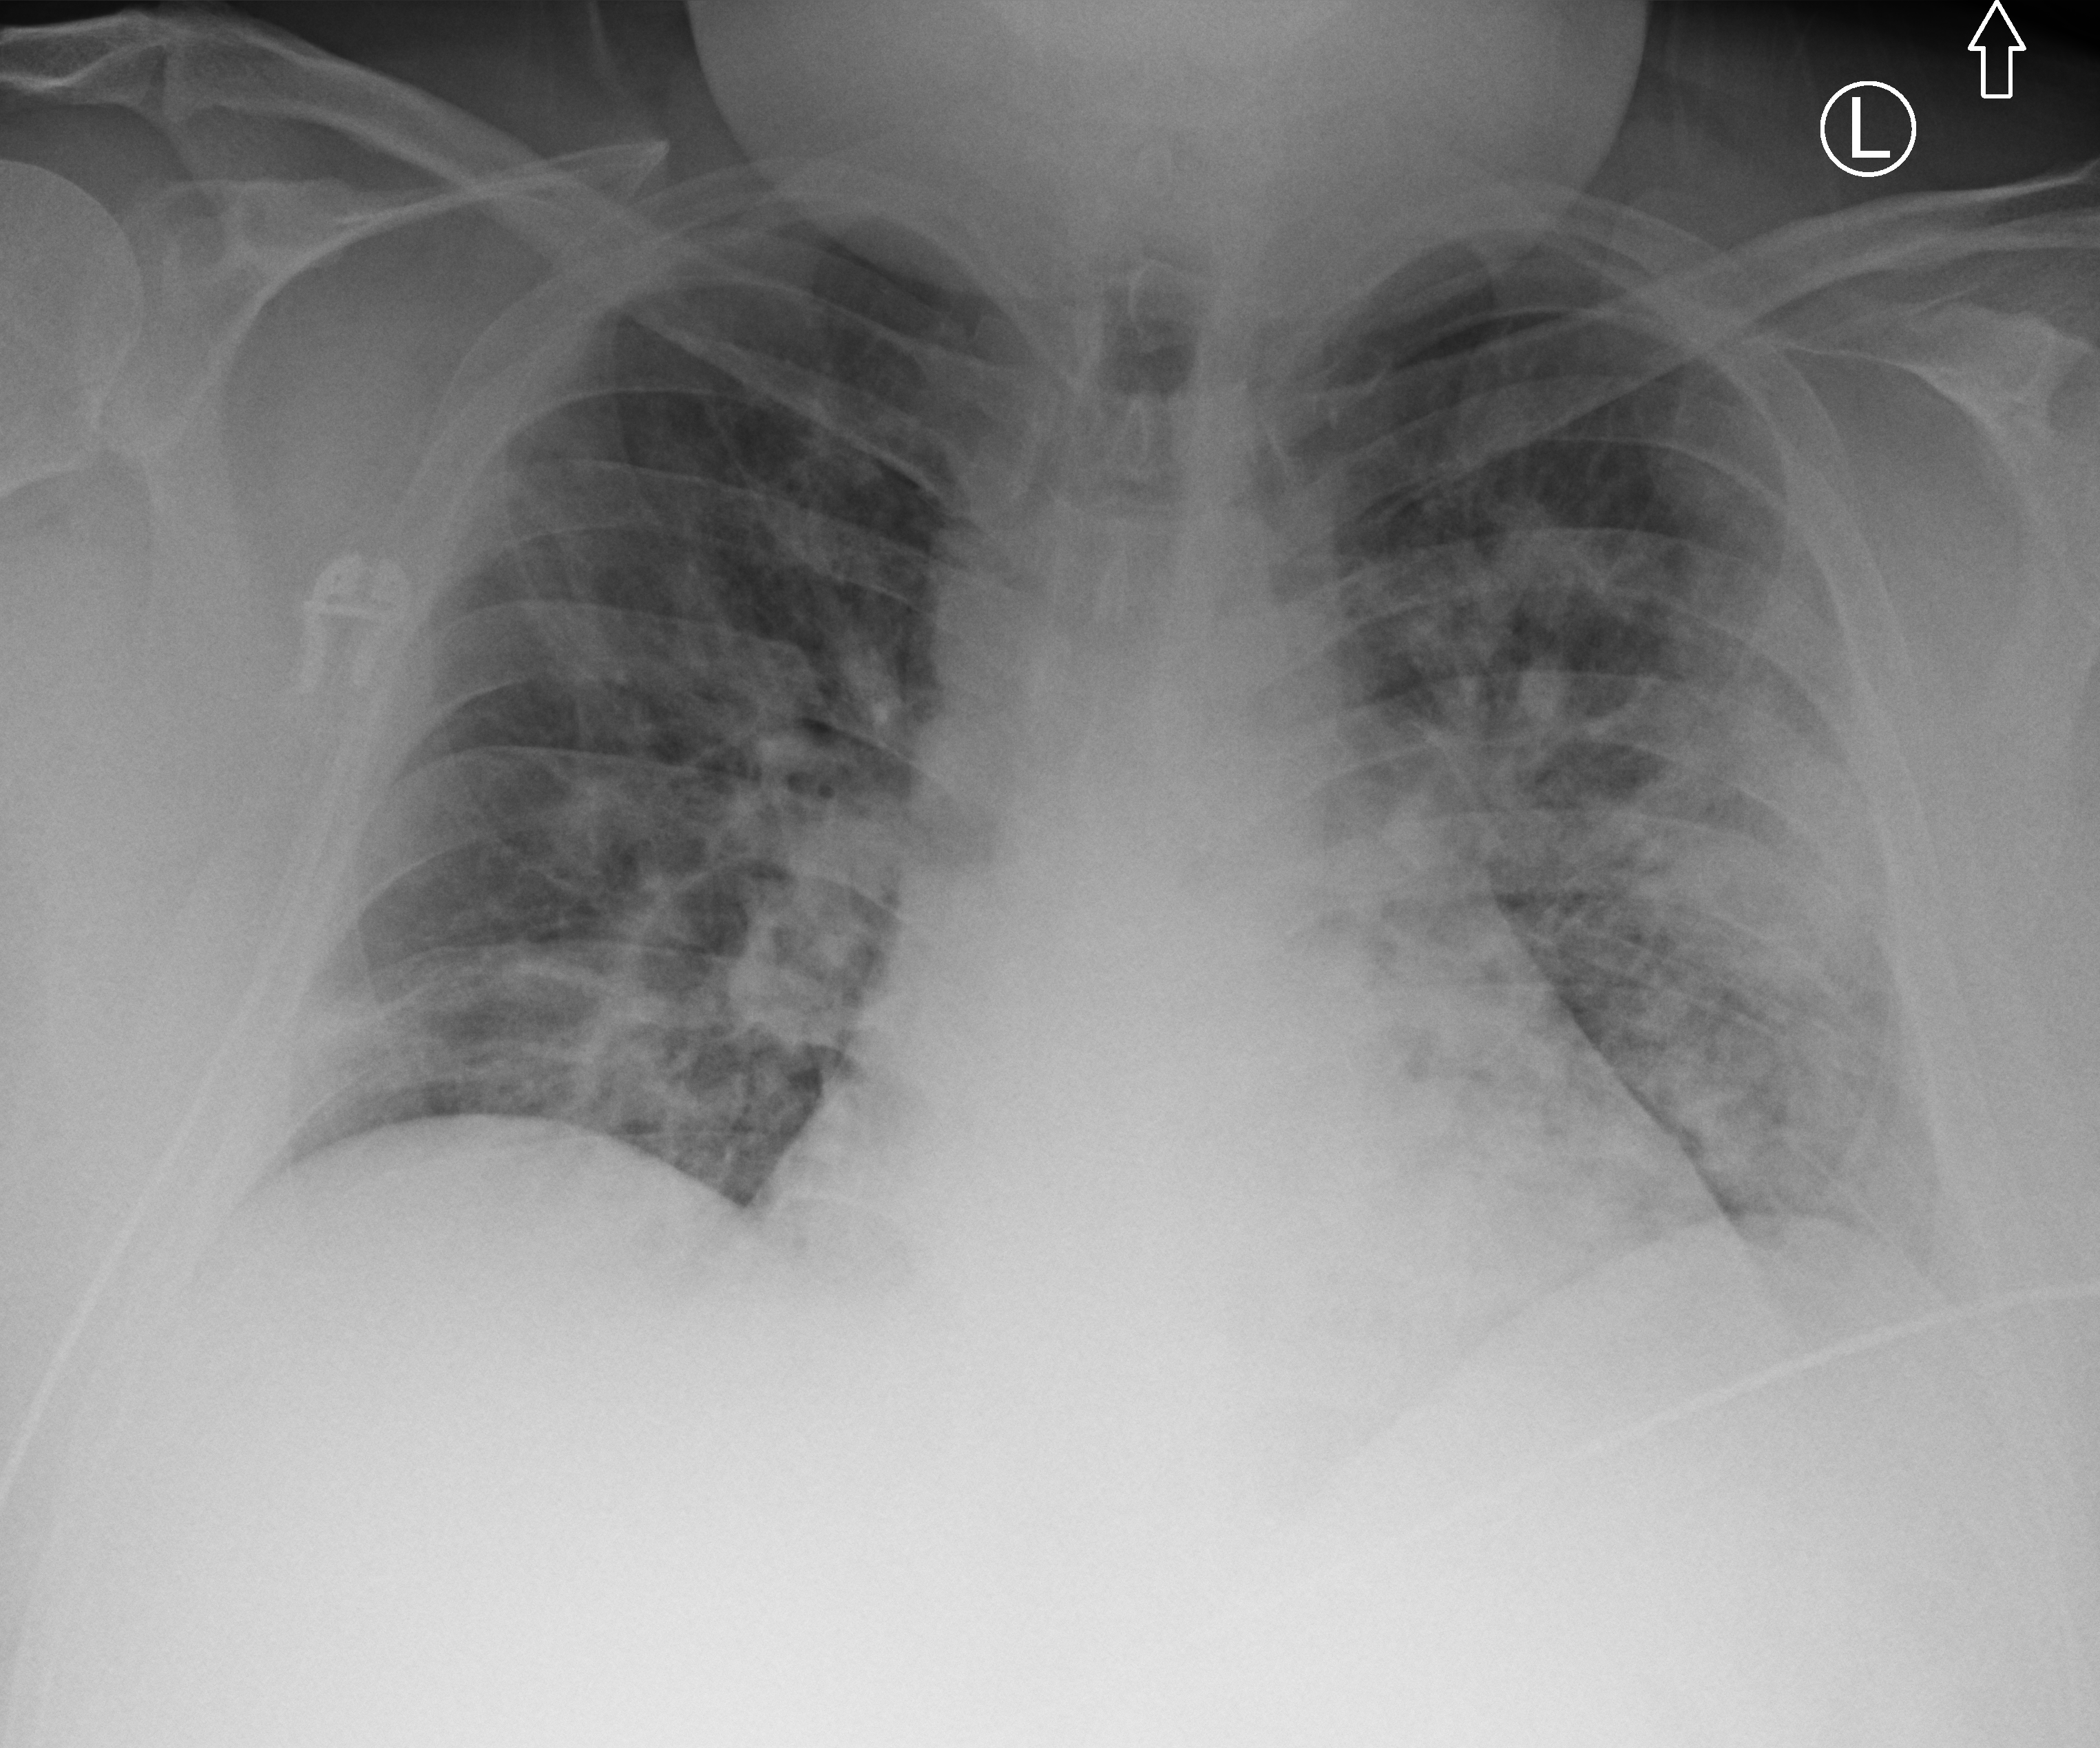
Chest X-ray (portable); anteroposterior (AP) projection. Patient hospitalised with COVID-19; male, aged 18–59 years.
Admission-level facts for this patient (not findings on this image; timing relative to this image not recorded): length of hospital stay: 20 days.